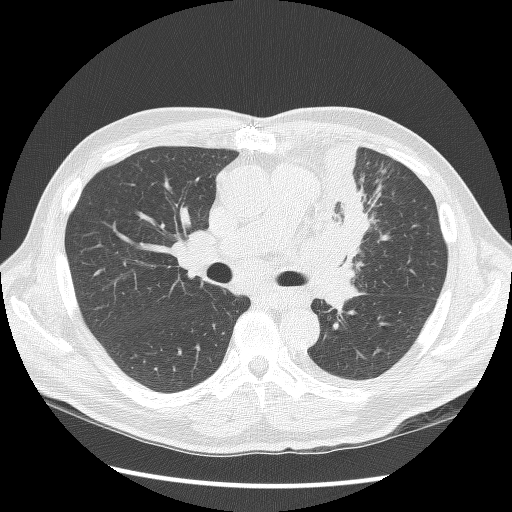
Chest CT (low-dose screening protocol), one axial image. Second annual screen. Lung window (W 1500 / L -600 HU). 2.5 mm slice thickness. Lung (sharp) reconstruction kernel (BONE). 120 kVp. Male, age 64 years at enrolment.
Expert-annotated lung lesion, bounding box (x1, y1, x2, y2) in pixels: (303, 144, 385, 283). No non-calcified nodule or mass ≥4 mm was recorded by the screening reader at this exam. Official screen result: positive, other.